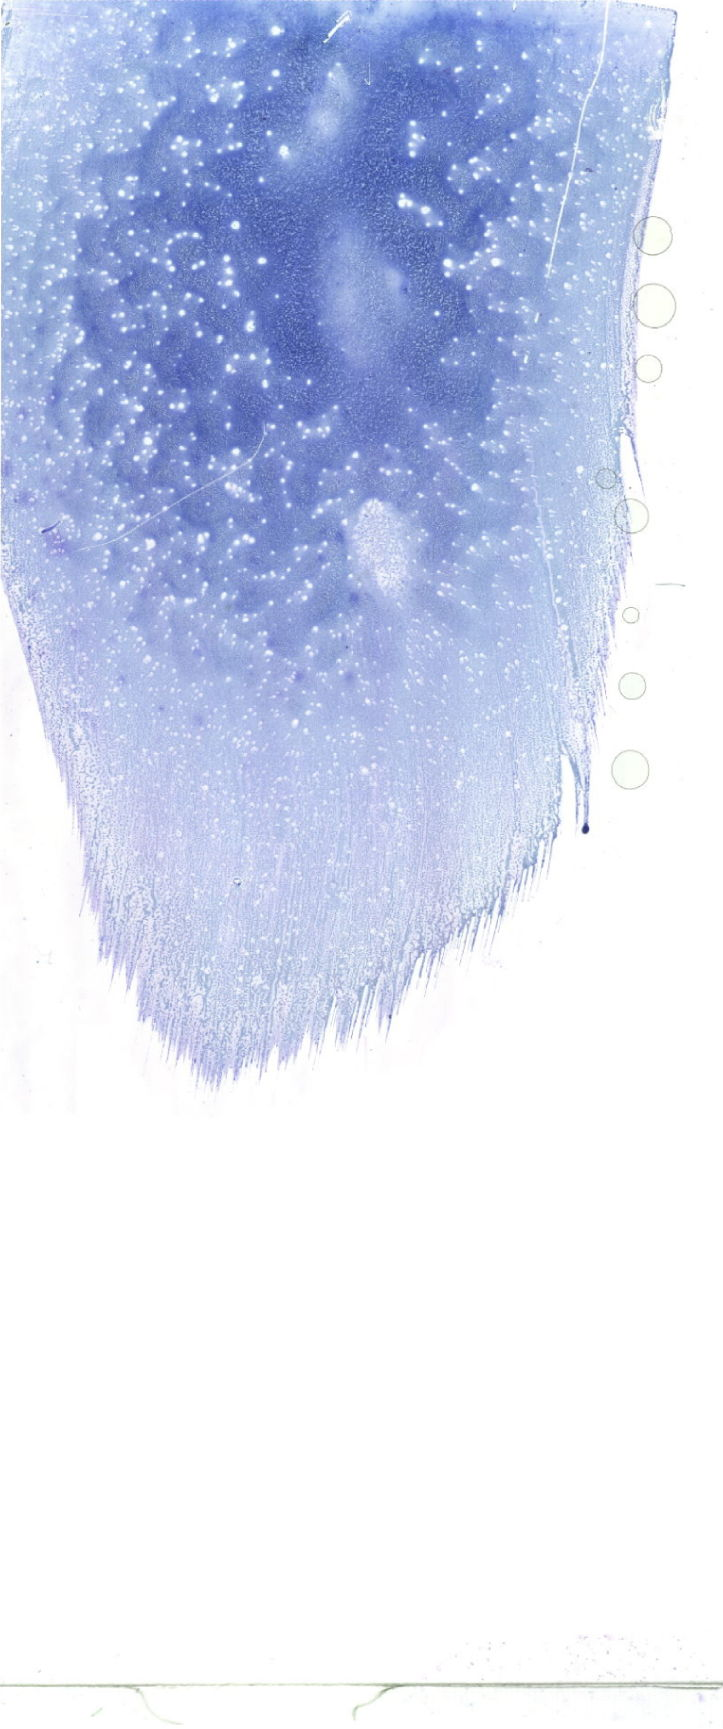
Whole-slide image of a May-Grünwald-Giemsa (MGG)-stained bone marrow aspirate smear, whole scanned area (about 20.5 x 49.0 mm) shown as a low-resolution overview. Male patient.
Diagnosis: Acute Myeloid Leukemia with Maturation.